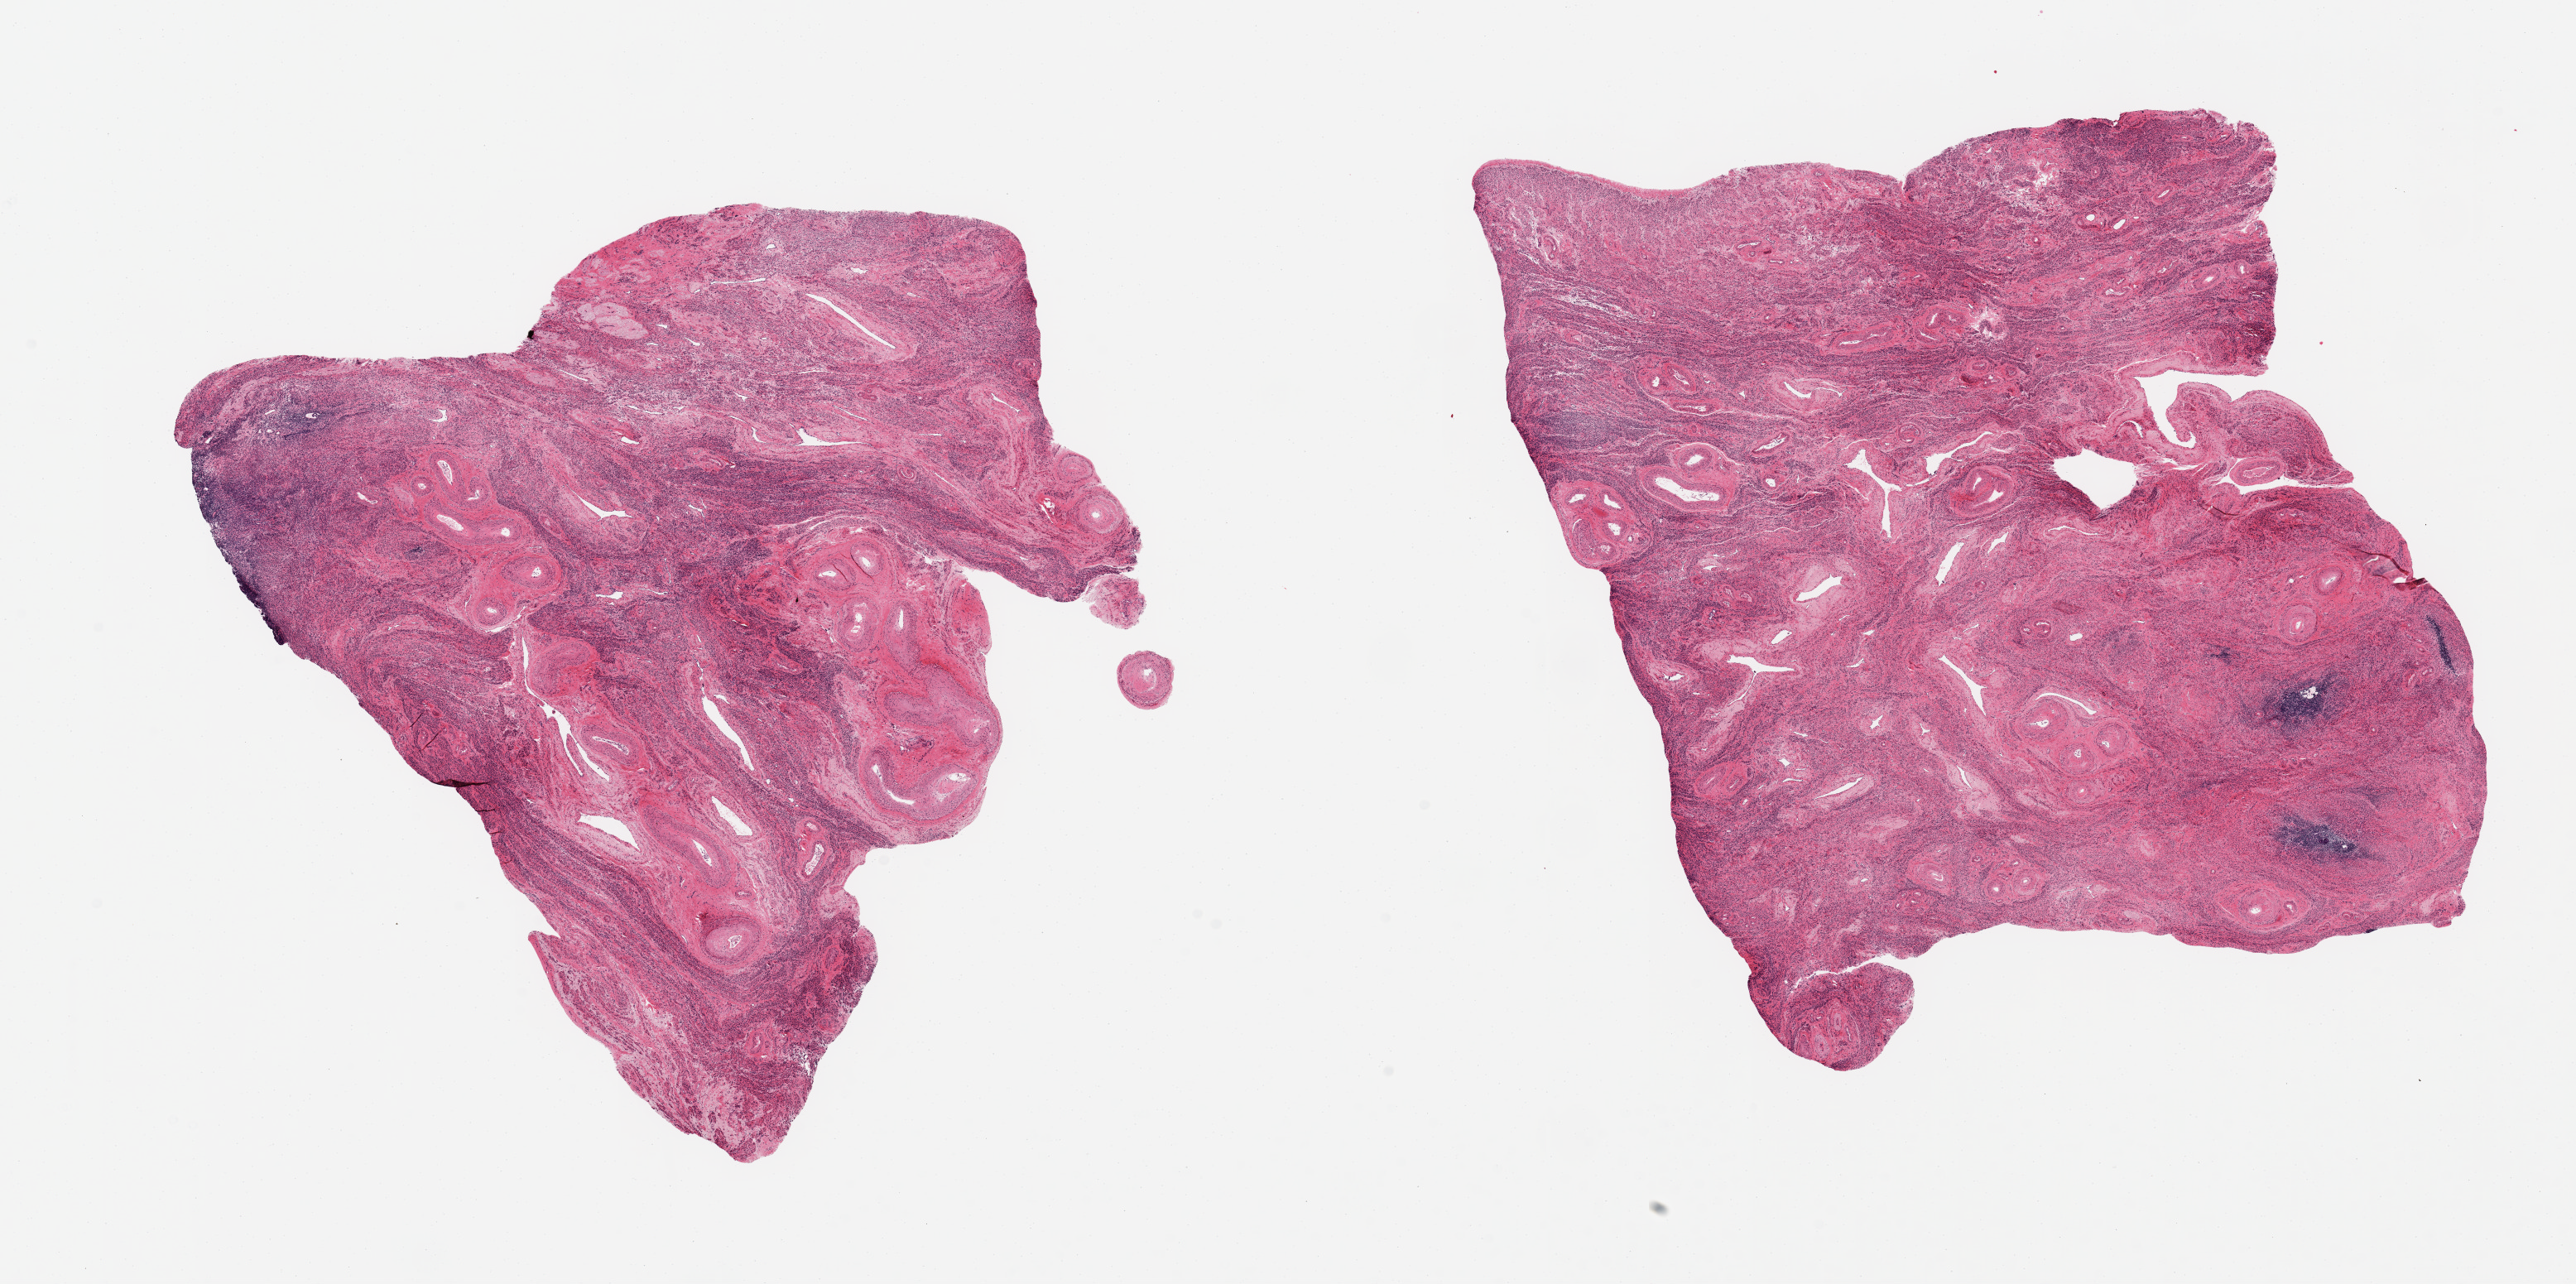
Whole-slide image, H&E stain, a low-resolution overview of the entire scanned area, about 24.6 x 12.3 mm, PAXgene-fixed paraffin-embedded (PFPE) section, sampled site (target tissue): uterus, tissue donor sample. Female donor.
* reviewer comment on this tissue sample: 2 pieces; mostly myometrium; atrophic endometrium